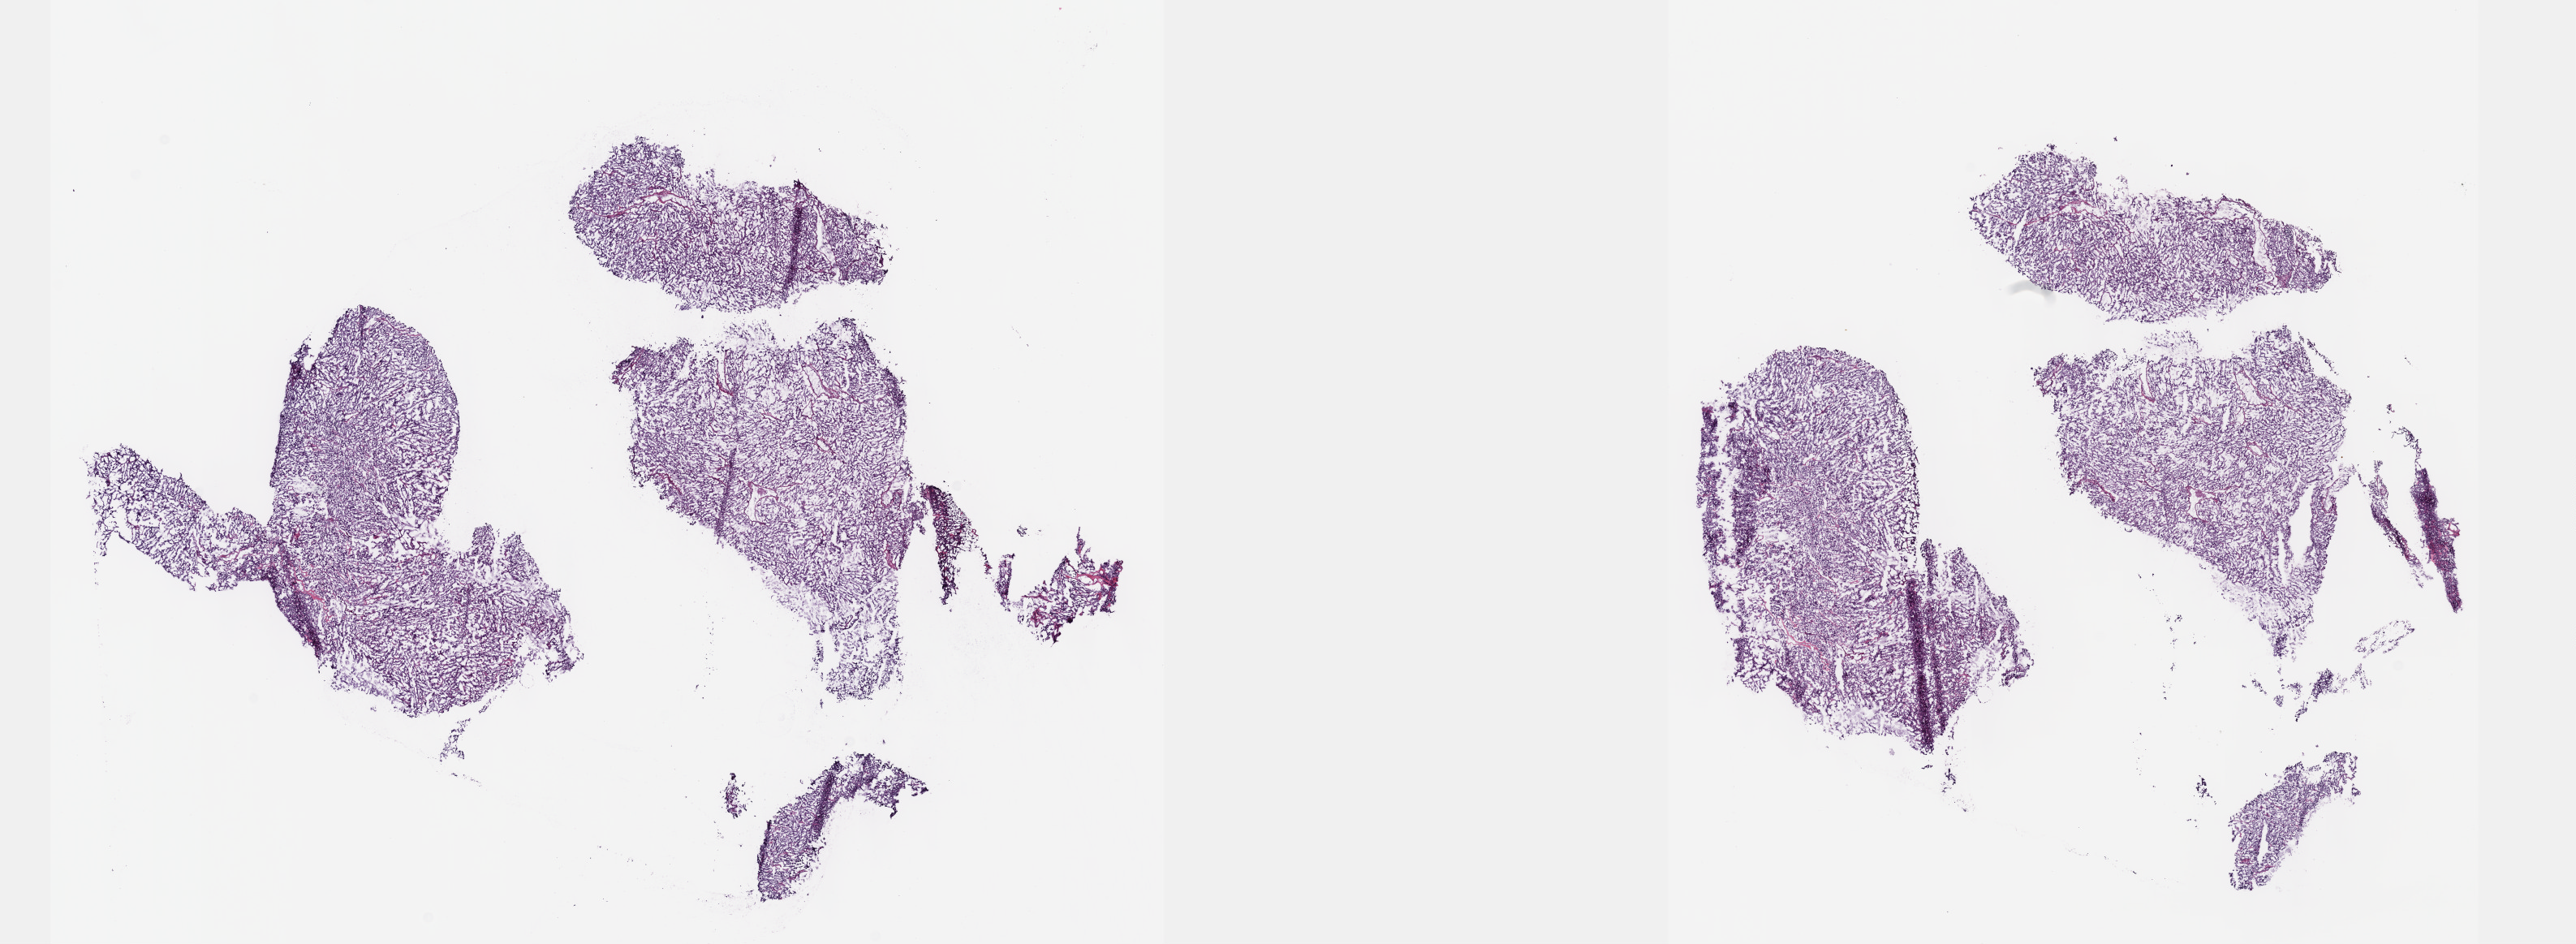
Digitized H&E-stained tissue section (whole slide), whole scanned area (about 25.7 x 9.4 mm, from a 40x scan) shown as a low-resolution overview. Frozen section from the top of the tissue portion. Primary tumour sample from the adrenal gland. Male patient; age at initial diagnosis 49 years. Slide review estimates, as recorded: tumour cells 95%, tumour nuclei 95%, normal cells 0%, stromal cells 5%, necrosis 0%. Inflammatory infiltration, as recorded: lymphocyte infiltration 0%, monocyte infiltration 0%, neutrophil infiltration 0%.
* pathologic diagnosis: Pheochromocytoma, NOS